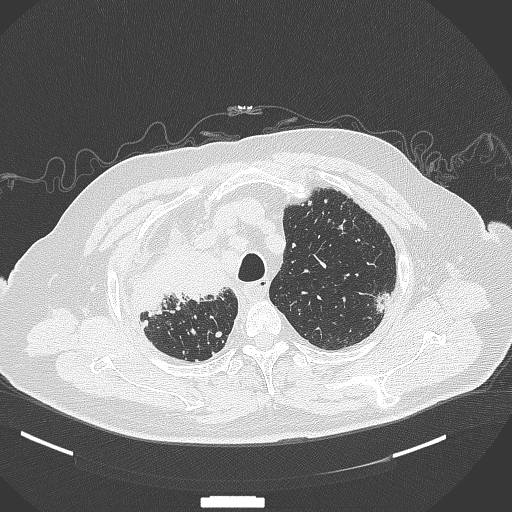
Chest CT, one axial slice. Slice 297 of 384 in the series (ordered by position). 120 kVp. Lung window (W 1500 / L -600 HU). 512 × 512 image matrix. Male patient, age 69 years. Case-level facts recorded for this patient, not image findings: clinical TNM (as recorded): T4 N3 M1.
Annotated regions visible in this slice (bounding box drawn by a radiologist):
- lung tumour (recorded histology: adenocarcinoma): bounding box [x1, y1, x2, y2] px = [135, 248, 230, 317]